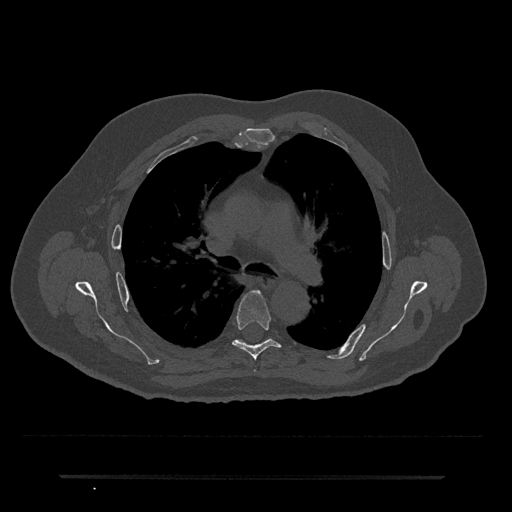
CT including the spine, one axial slice. Slice 481 of 797 in the series (ordered by position). Reconstruction kernel Br40s/3. Bone window (W 1800 / L 400 HU). 512 × 512 image matrix. Patient: male, 69 years. Case-level facts recorded for this patient, not image findings: primary cancer: prostate.
Outlined on this slice (semi-automatic segmentation, software-assisted and operator-edited):
- T5 vertebra: box from (x=232, y=290) to (x=290, y=360) px